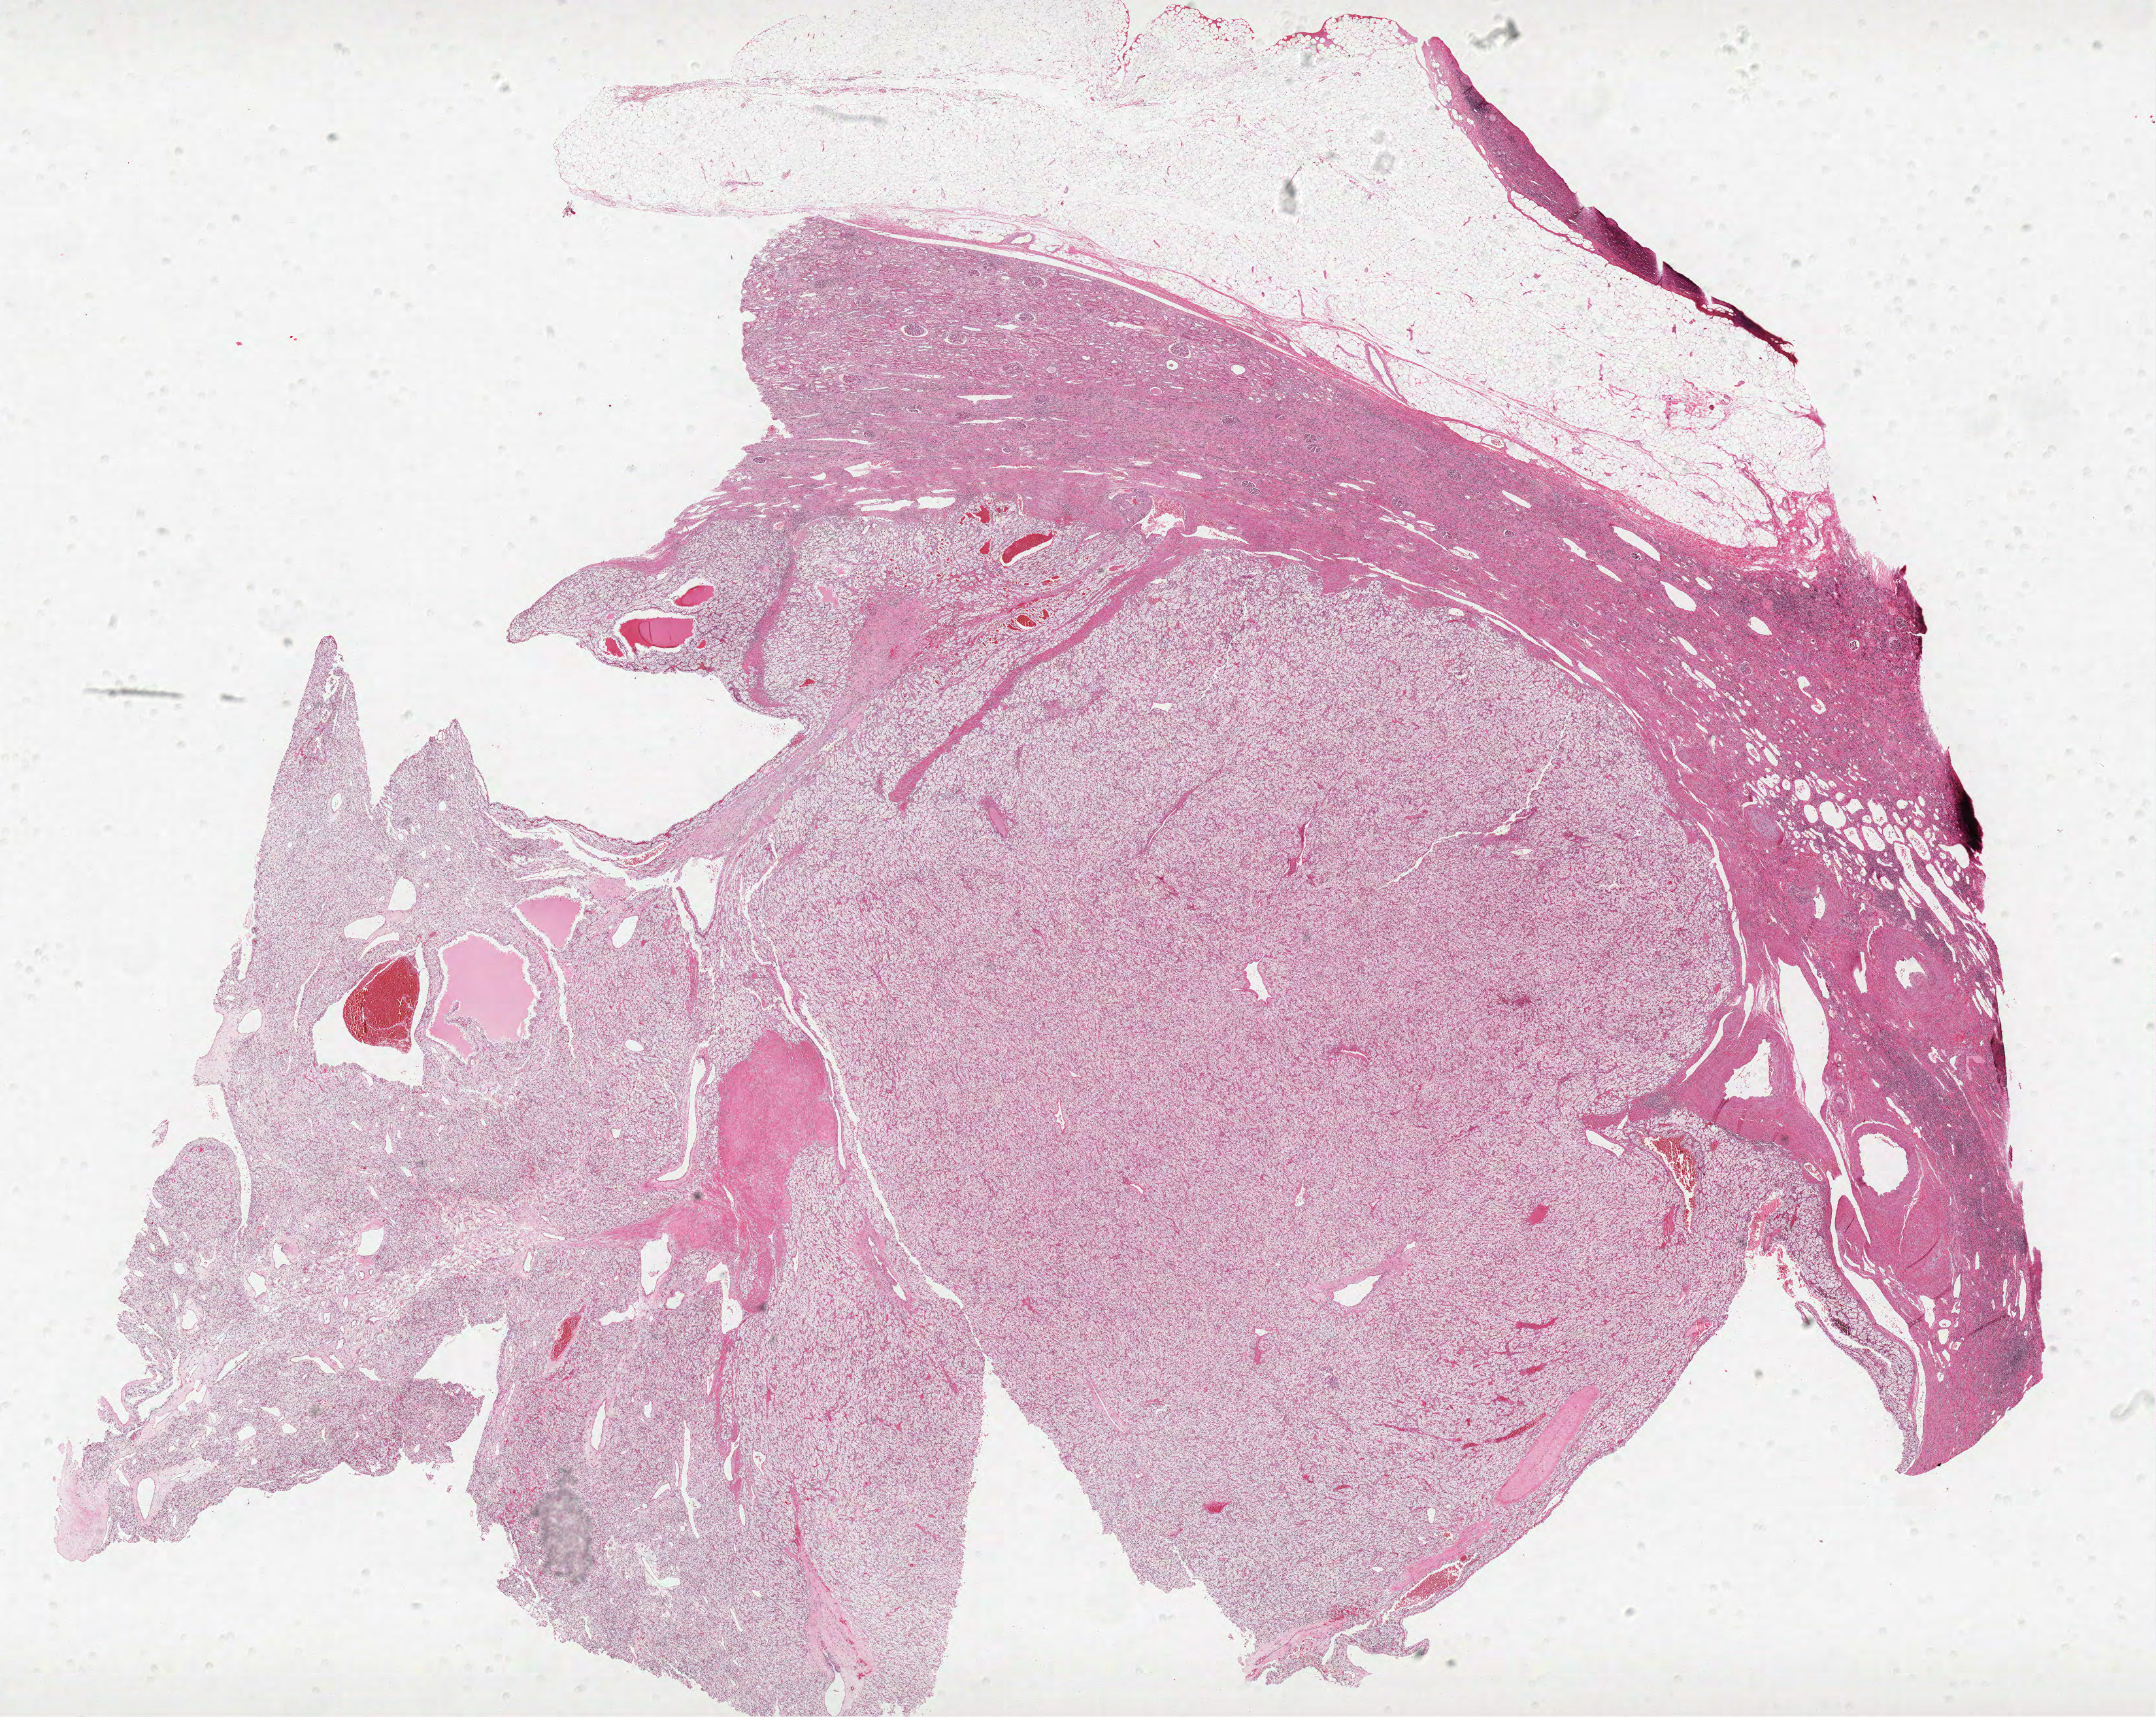
H&E-stained whole-slide image, a low-resolution overview of the entire scanned area, about 26.4 x 21.0 mm; formalin-fixed paraffin-embedded (FFPE) diagnostic section; kidney, primary tumour sample. Female, age 51 years at initial diagnosis.
Pathologic diagnosis: Clear cell adenocarcinoma, NOS.